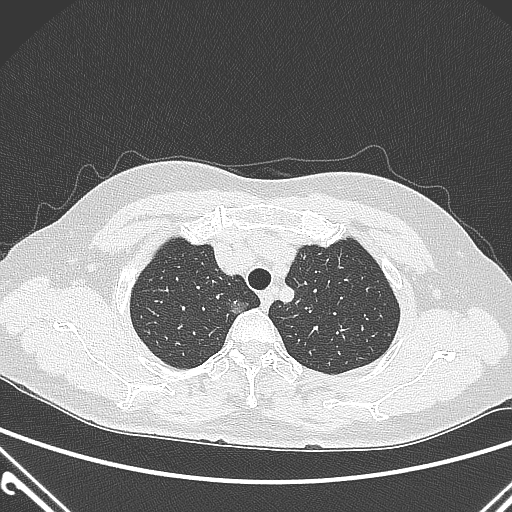
Chest CT, one axial slice. Slice 237 of 300 in the series (ordered by position). 120 kVp. Lung window (W 1500 / L -600 HU). 512 × 512 image matrix, field of view 350 × 350 mm. Patient: female, 54 years. Case-level facts recorded for this patient, not image findings: clinical TNM (as recorded): T1a N0 M0.
Outlined on this slice (bounding box drawn by a radiologist):
- lung tumour (recorded histology: adenocarcinoma): bounding box (x1, y1, x2, y2) in pixels: (224, 296, 254, 321)